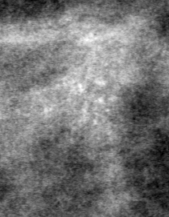
Region of interest cut from a scanned film mammogram (one marked finding), left breast, MLO view, BI-RADS breast density category 4 (scale 1–4).
- Calcifications, morphology pleomorphic, distribution clustered; BI-RADS assessment category 4; pathology (as recorded): malignant.